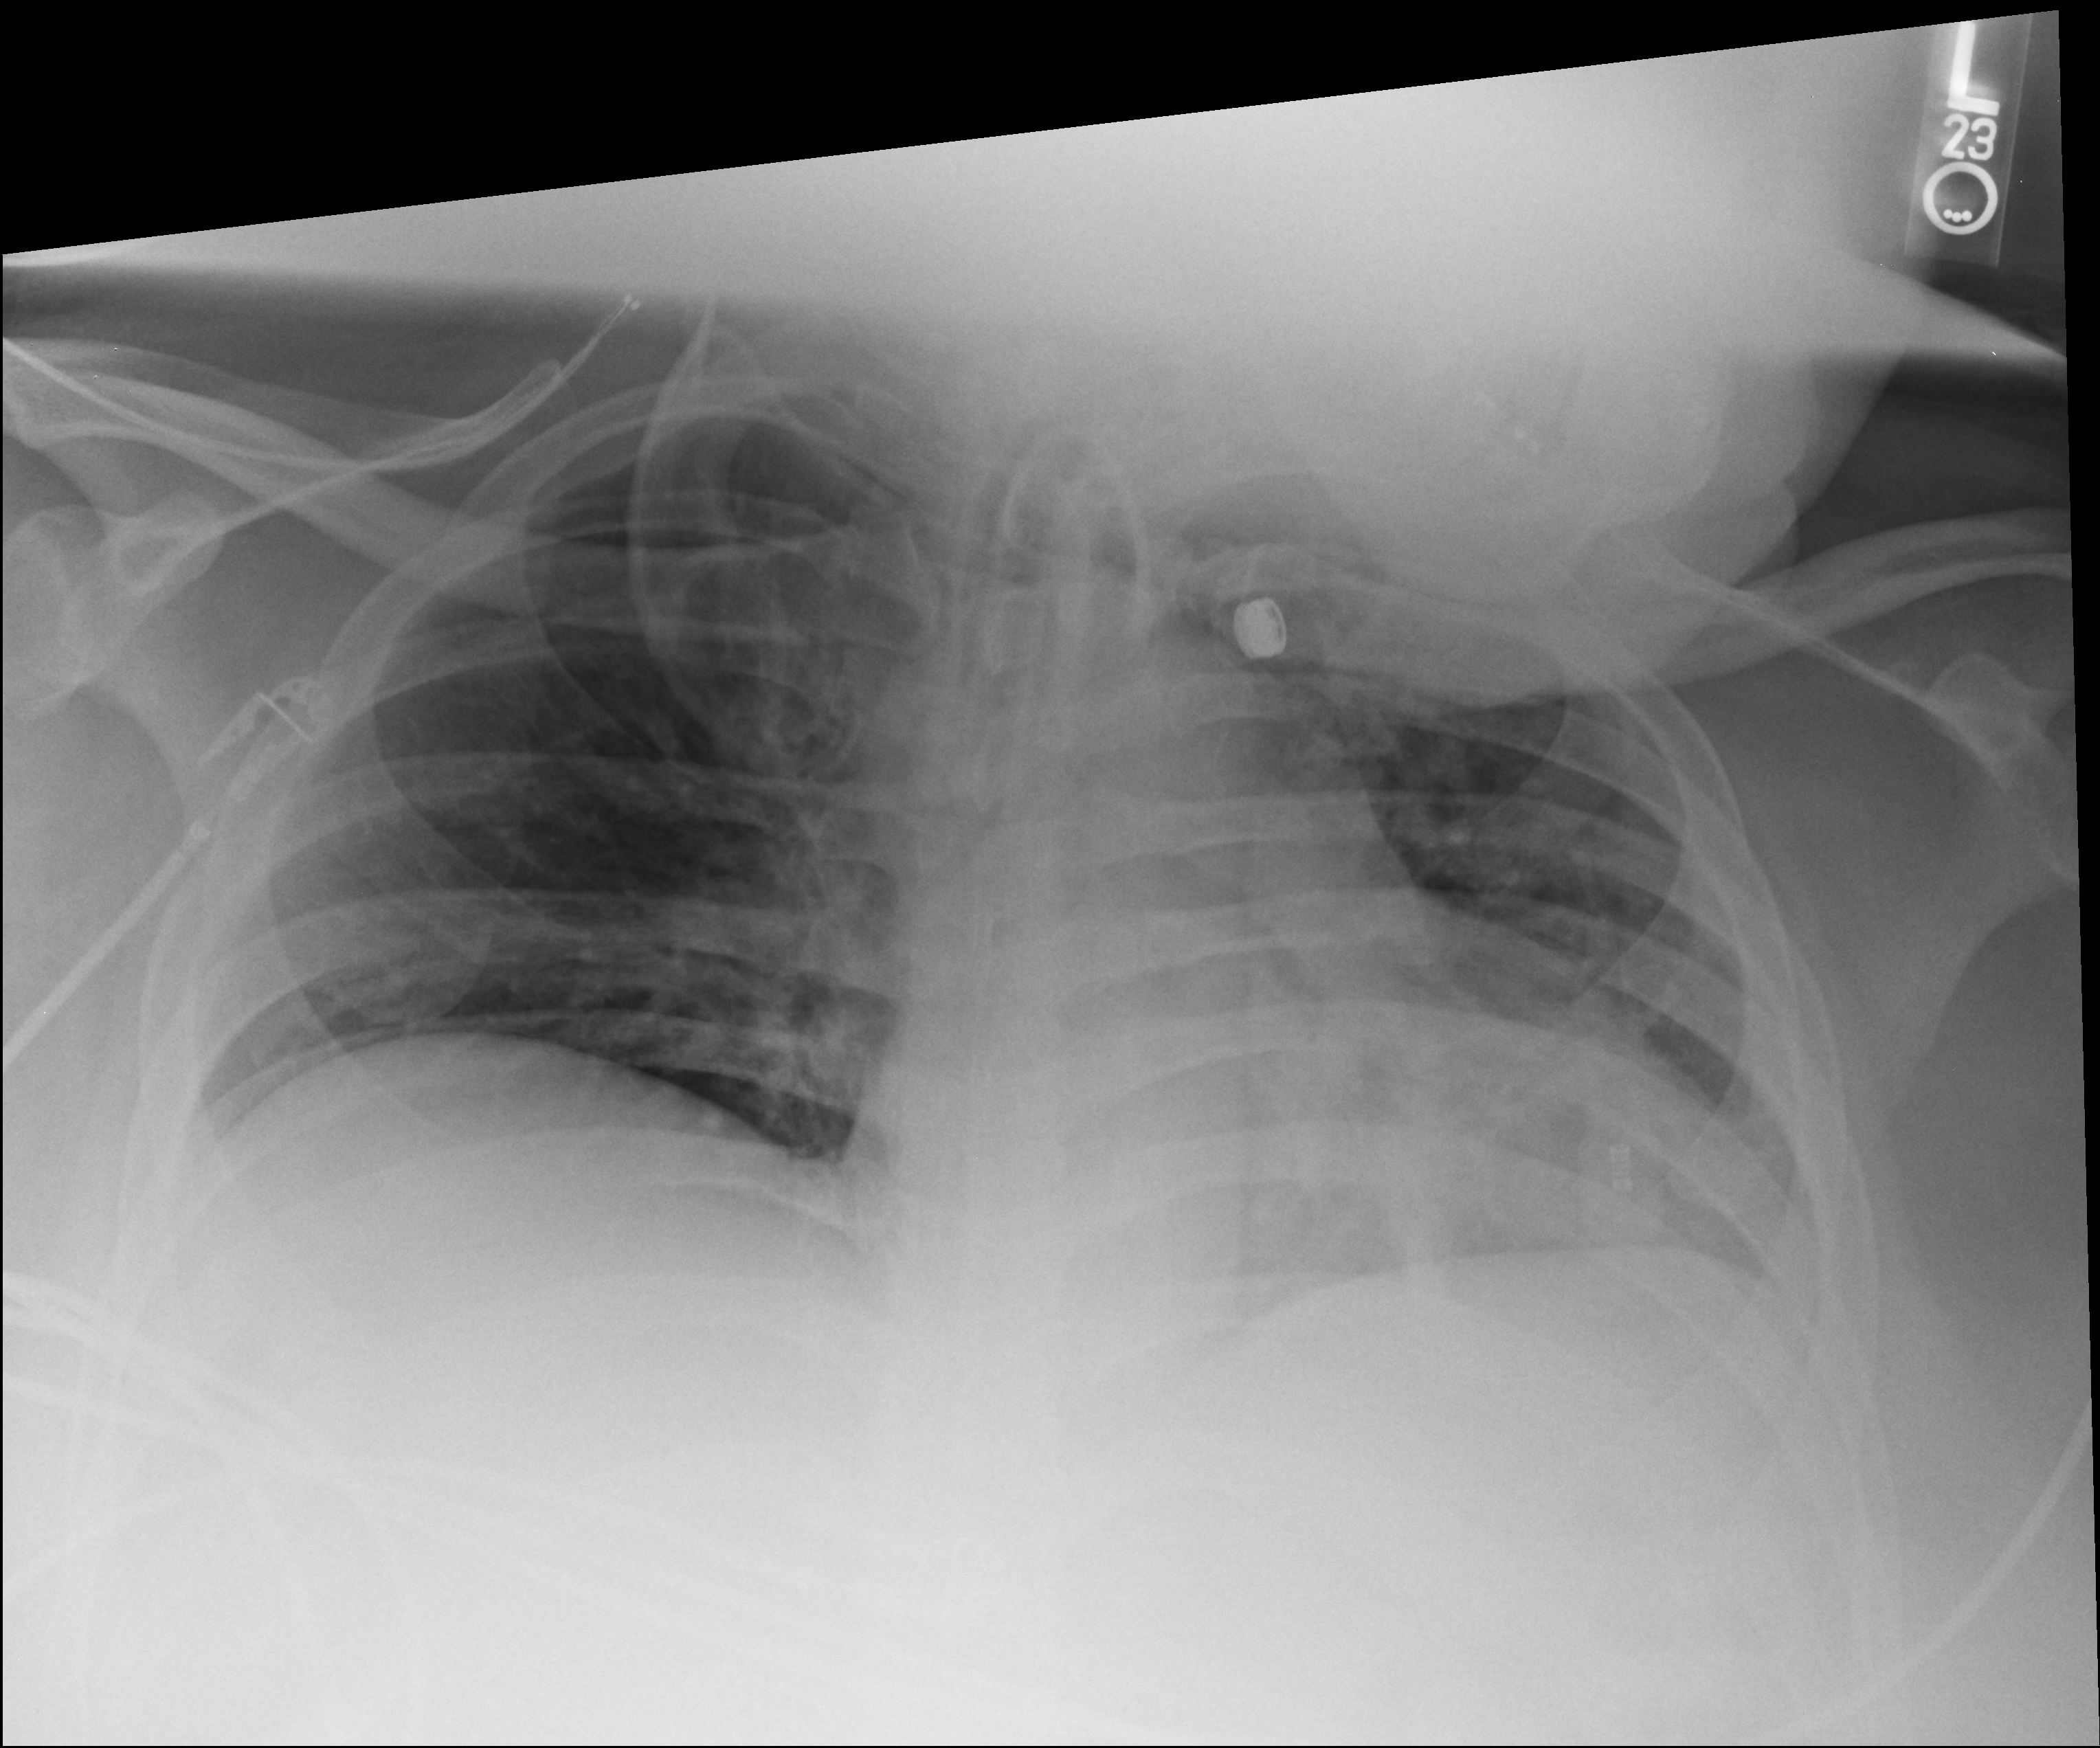
Bedside chest radiograph (computed radiography), anteroposterior (AP) projection. Male patient hospitalised with COVID-19, age 18–59 years.
Hospital-stay facts (about this admission, not read from this image; timing relative to this image not recorded): mechanically ventilated during this hospital stay: yes.